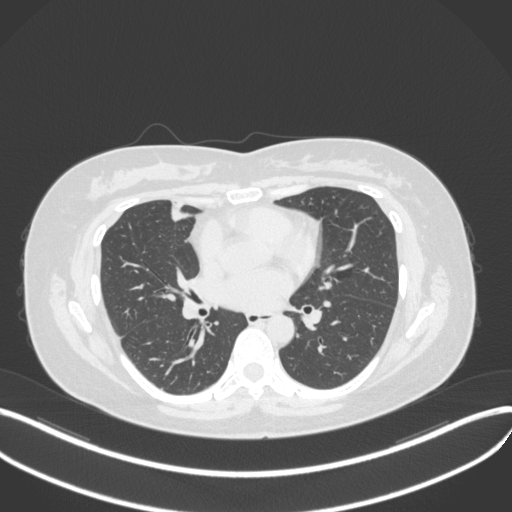
Chest CT, one axial slice. Position 156 of 272 along the scan axis. Lung window (W 1500 / L -600 HU). 512 × 512 image matrix, field of view 400 × 400 mm. Patient: female, 42 years. From the clinical record (not read from this slice): clinical TNM (as recorded): T1b N0 M0.
Annotated regions visible in this slice (bounding box drawn by a radiologist):
- lung tumour (recorded histology: adenocarcinoma): bounding box (x1, y1, x2, y2) in pixels: (169, 200, 196, 225)